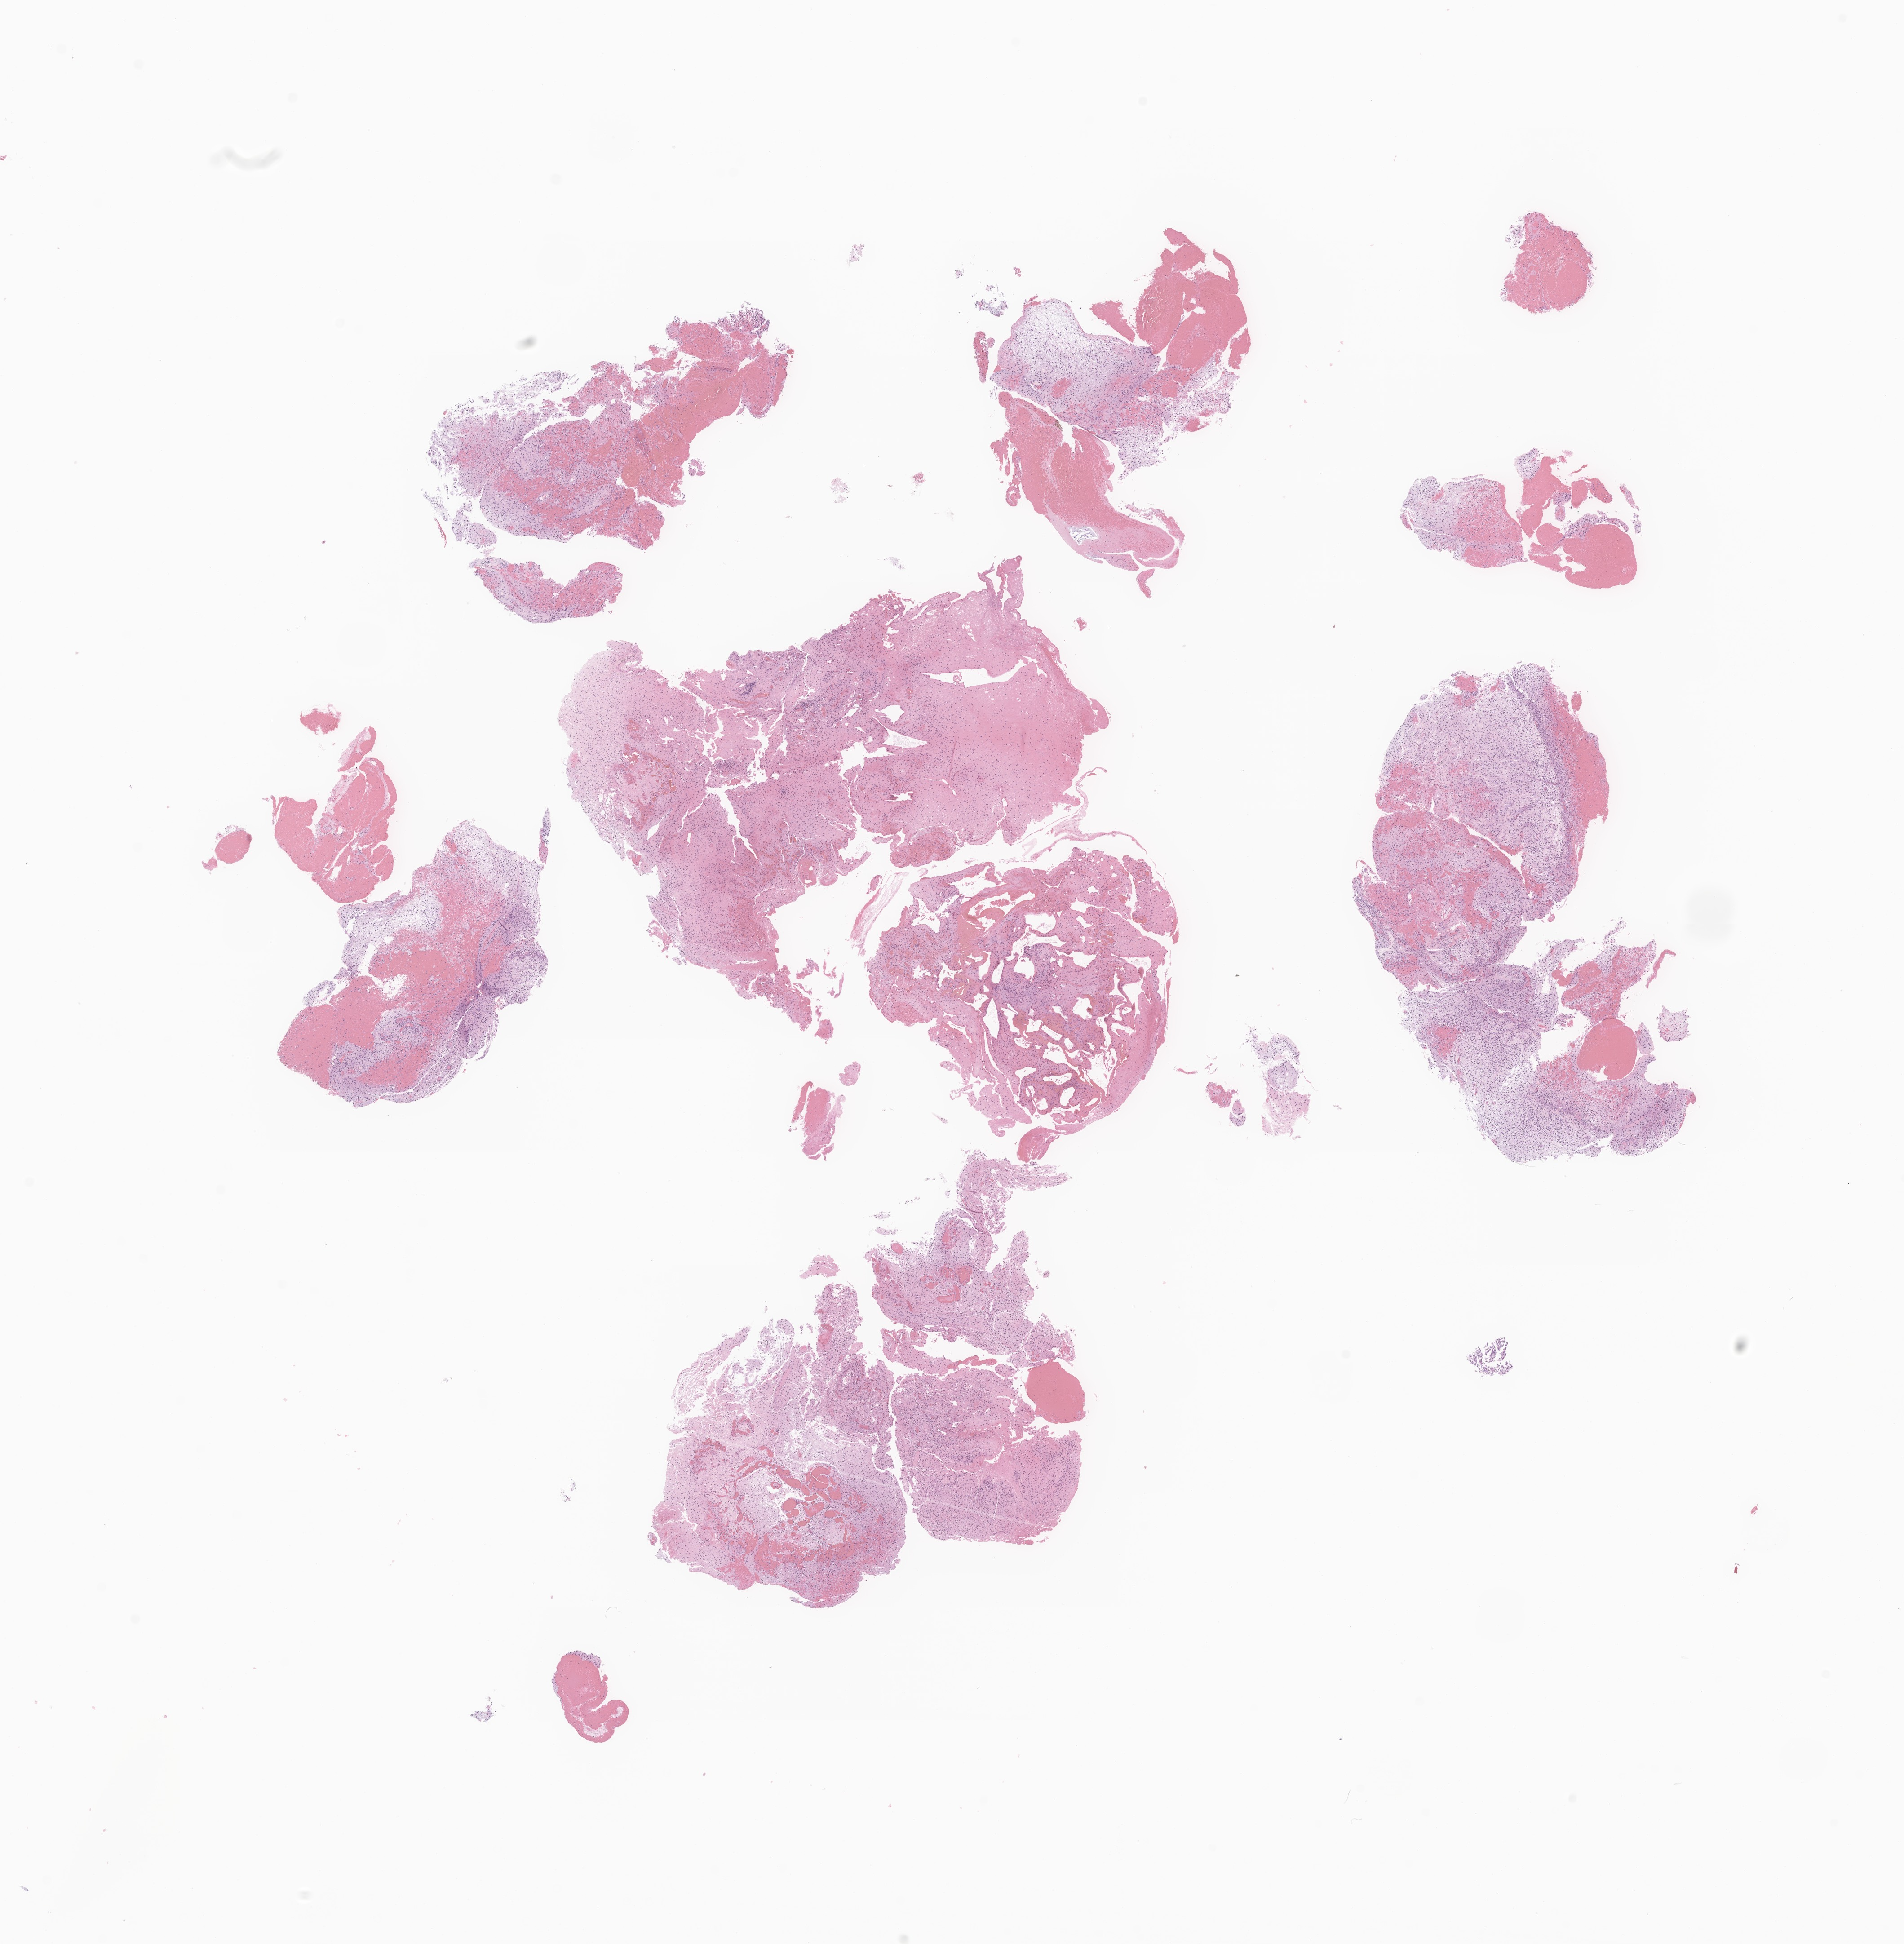
Haematoxylin and eosin whole-slide image of tumor tissue from the brain, whole scanned area (about 17.9 x 18.2 mm) shown as a low-resolution overview; formalin-fixed paraffin-embedded section. Female patient, age 133 months (11 years 1 month).
- recorded diagnosis: Pilocytic astrocytoma